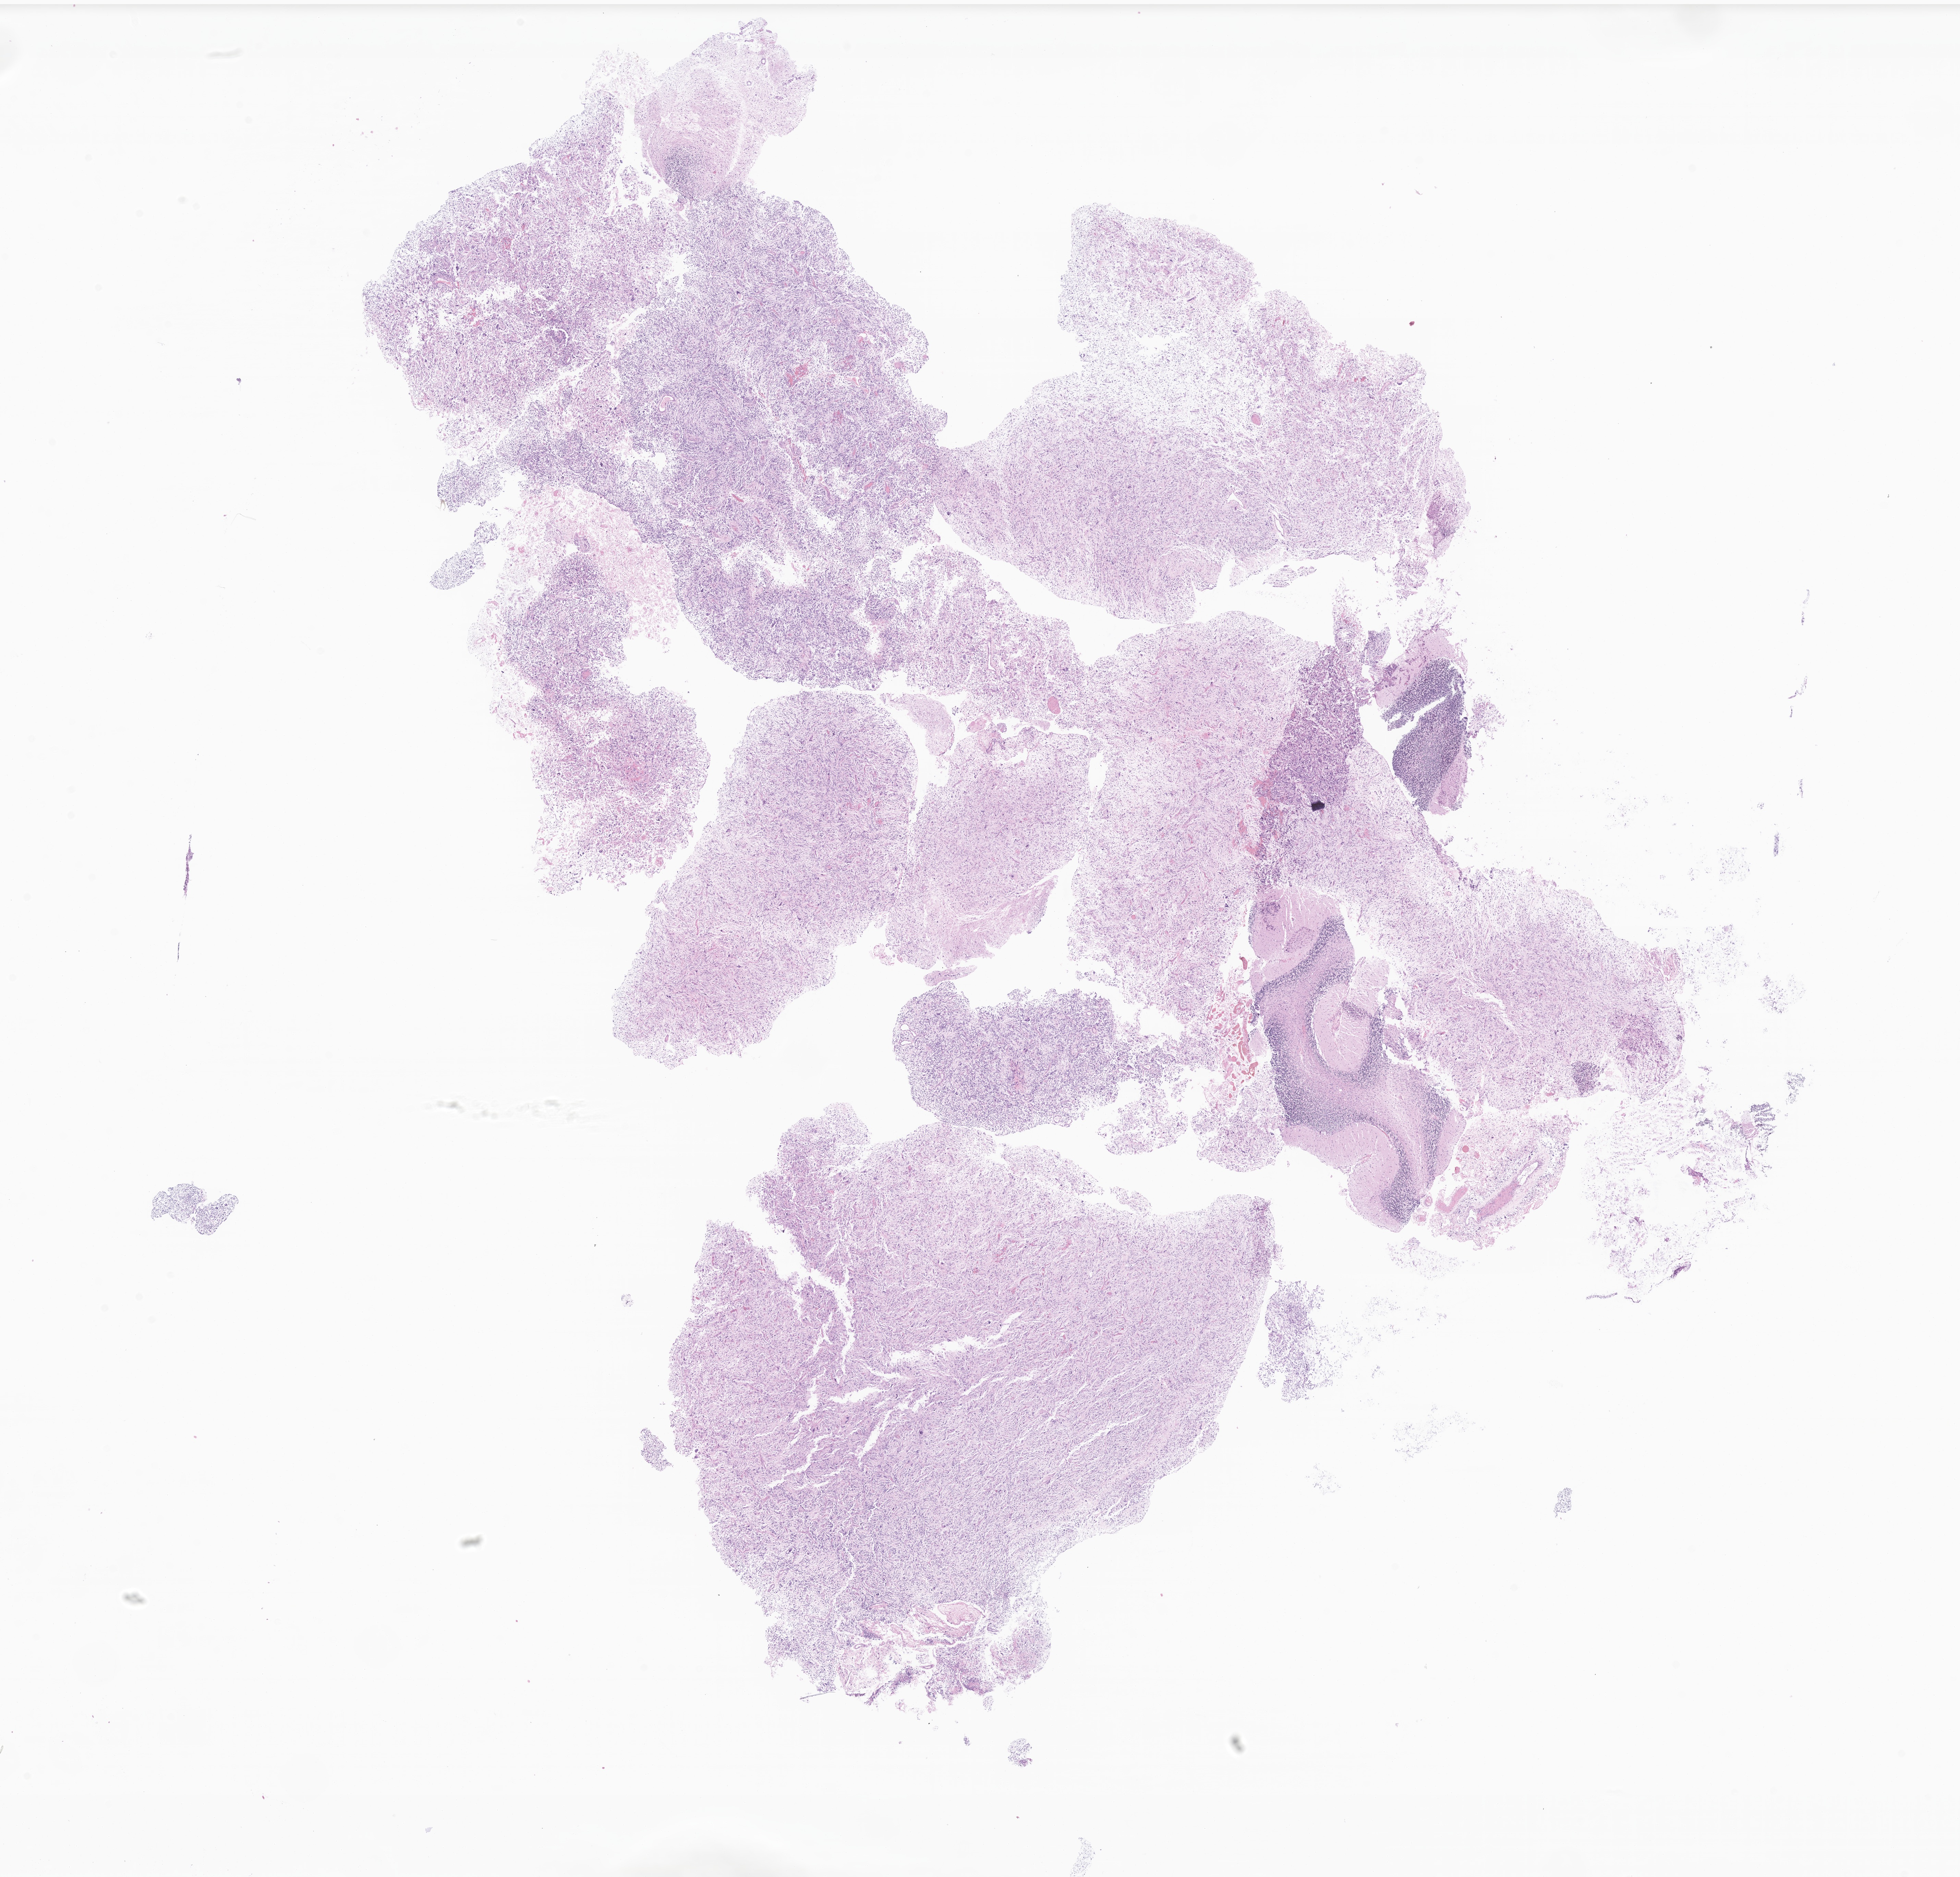
Digitized haematoxylin and eosin-stained section of tumor tissue from the cerebellum — shown as a low-resolution overview of the whole scanned area (about 24.1 x 23.1 mm); formalin-fixed, paraffin-embedded (FFPE) tissue. Patient male; age 167 months (13 years 11 months).
Diagnosis (ICD-O-3 morphology term): Glioma, malignant.